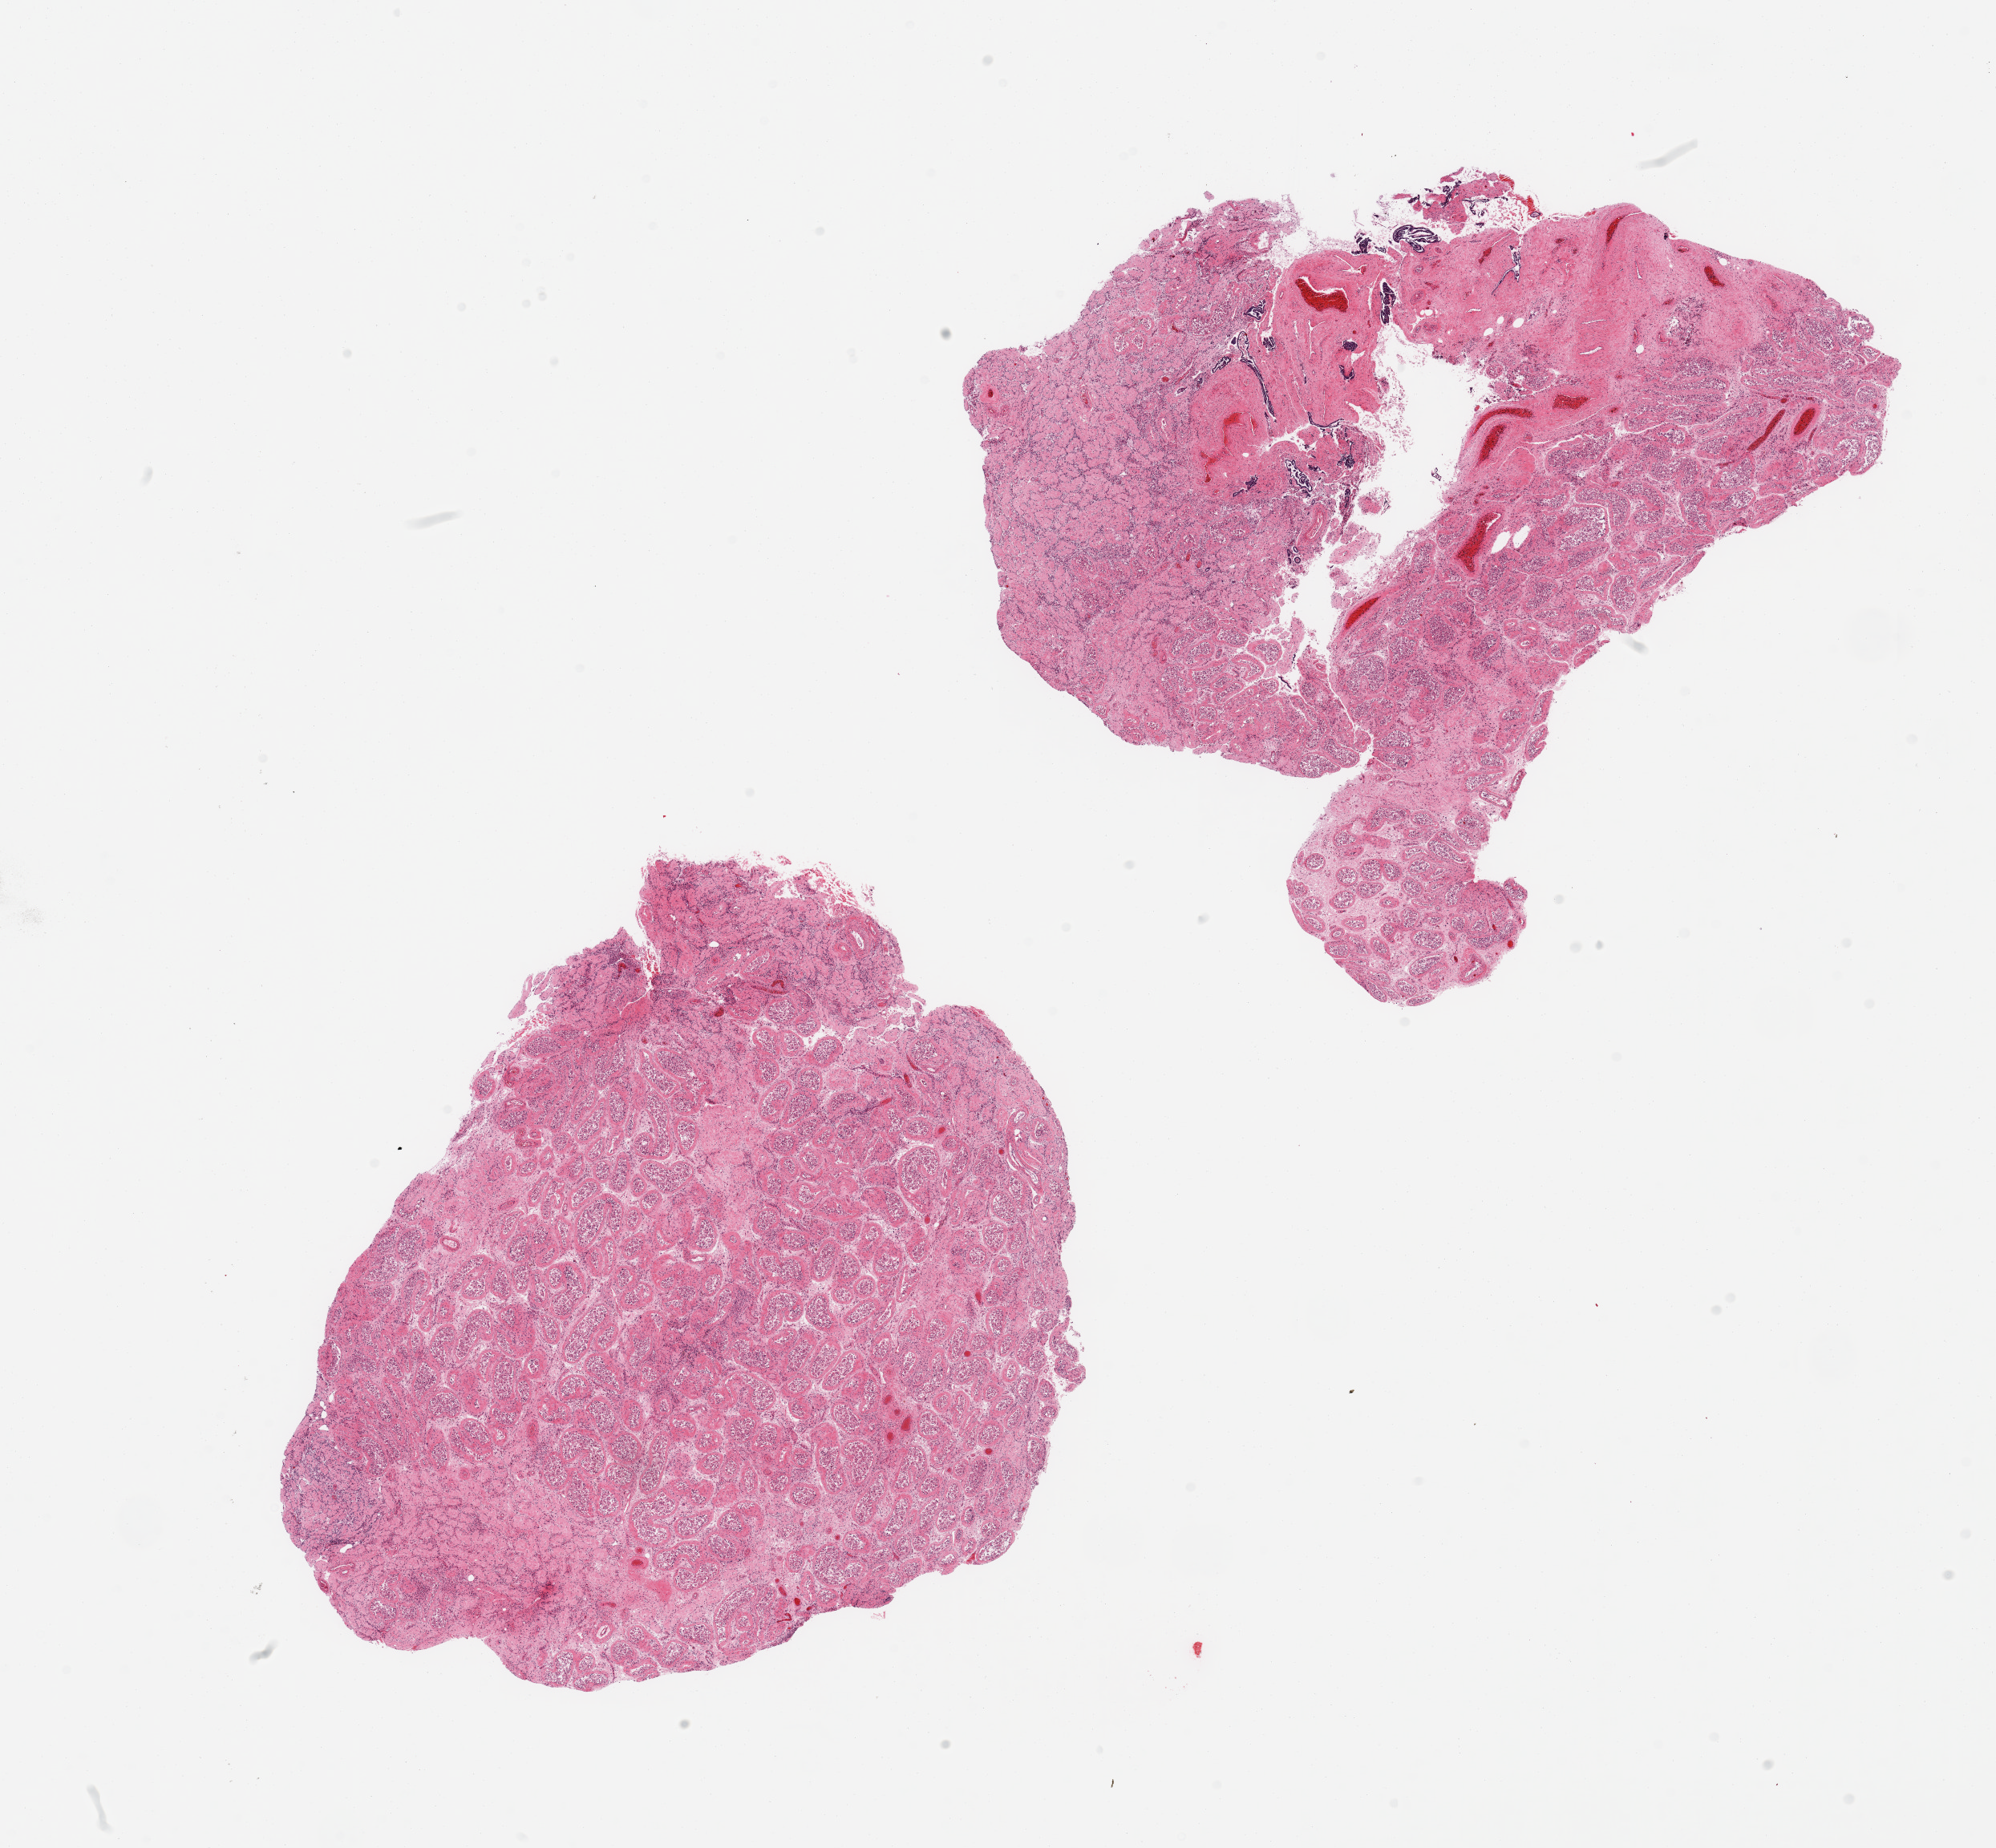
Digitized haematoxylin and eosin-stained section, brightfield — whole scanned area (about 19.7 x 18.2 mm, acquisition: 20x scan) shown as a low-resolution overview, PAXgene-fixed paraffin-embedded (PFPE) section, sampled site (target tissue): testis, donor tissue sample. Male donor.
• review note (as recorded): 2 pieces; atrophy with tubular hyalinization, portion of appendix testis